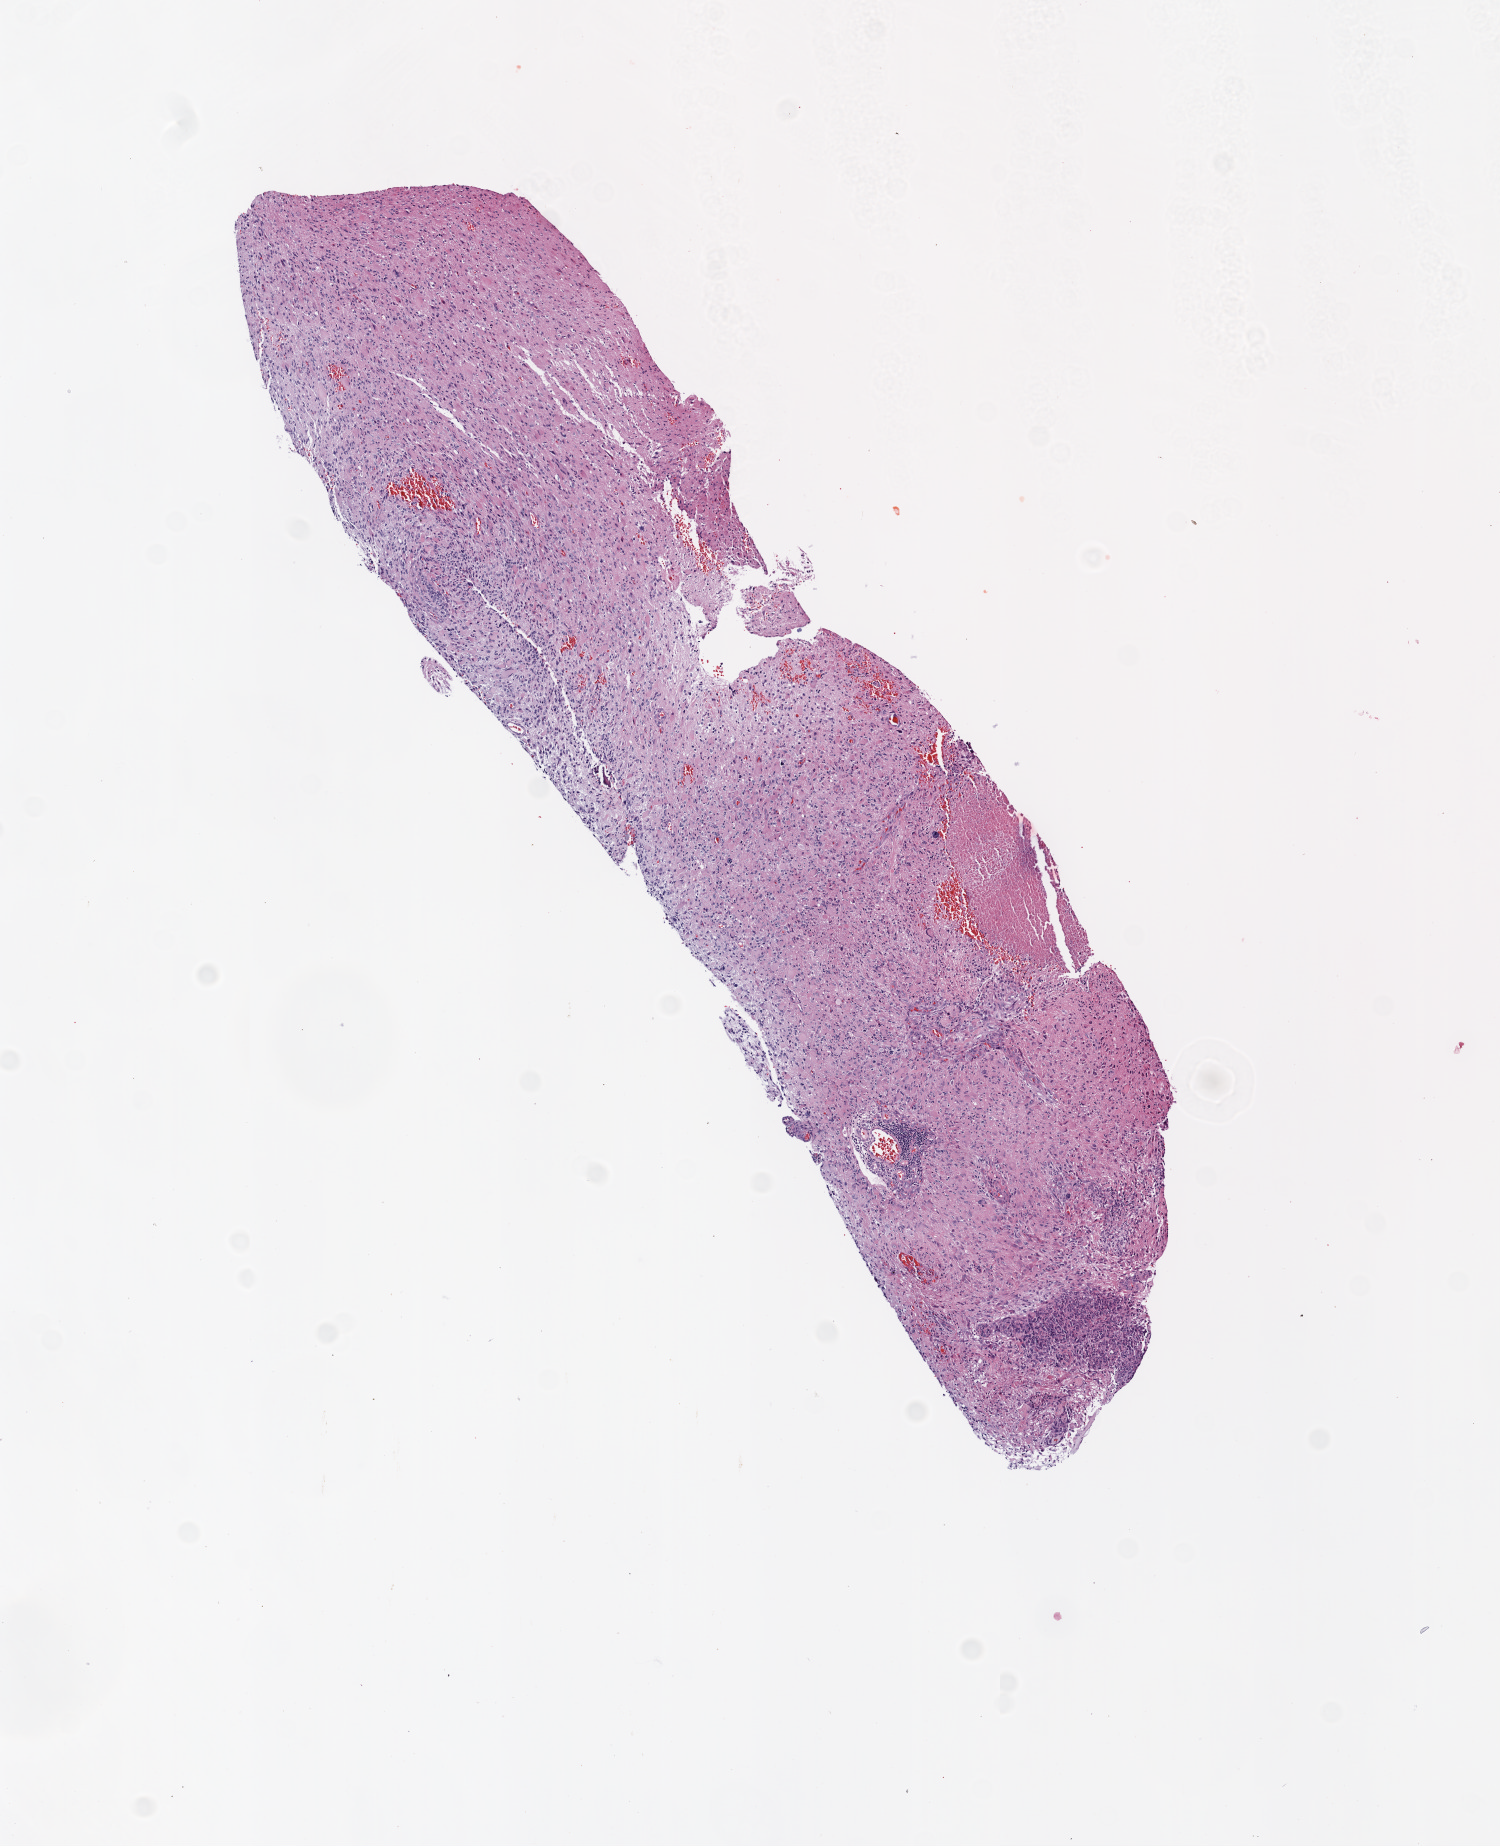
Hematoxylin and eosin (H&E) stained whole-slide image — whole scanned area (about 6.0 x 7.4 mm, slide scanned at 20x) shown as a low-resolution overview, formalin-fixed paraffin-embedded (FFPE) diagnostic section, brain, primary tumour sample. Patient: male, age at initial diagnosis 46 years.
• diagnosis: Glioblastoma